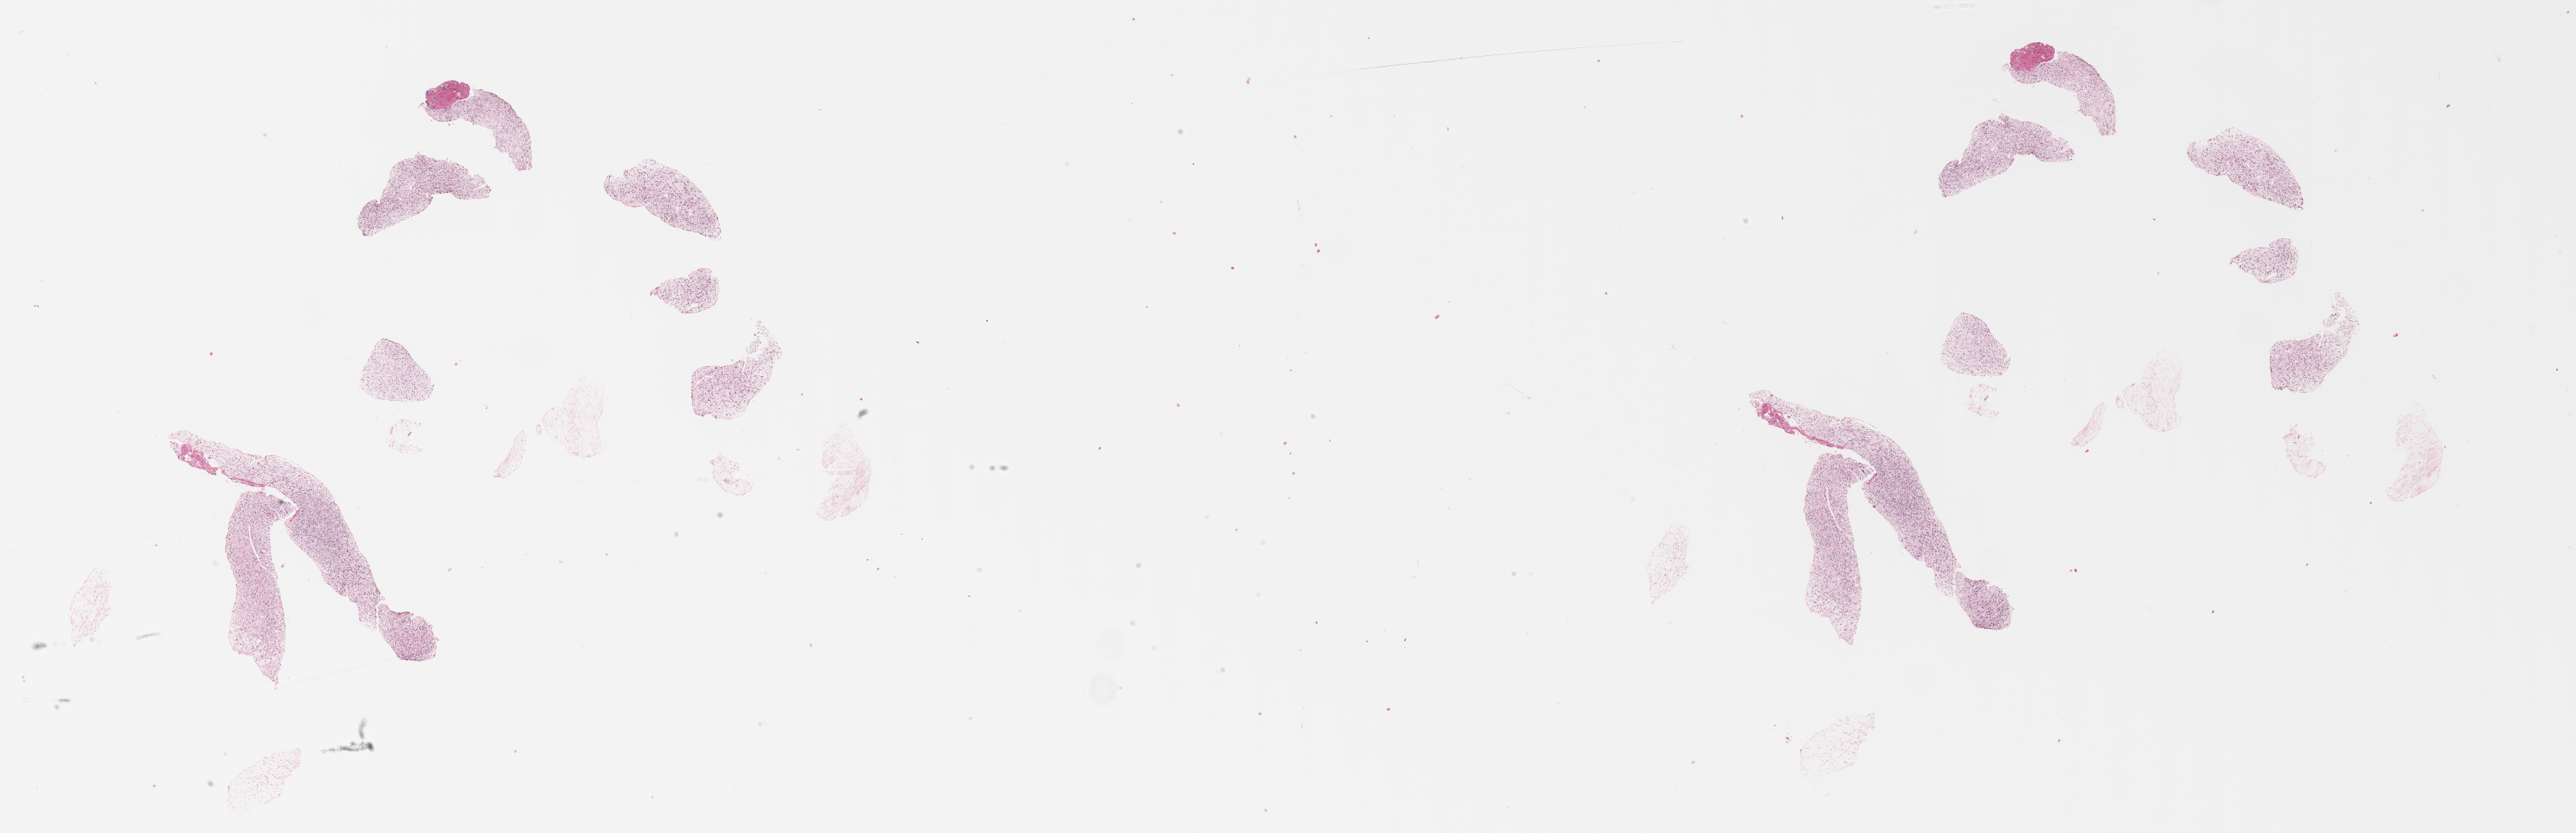
Whole-slide image, hematoxylin and eosin (H&E) stain of tumor tissue — whole scanned area (about 28.7 x 9.3 mm) shown as a low-resolution overview; formalin-fixed, paraffin-embedded (FFPE) tissue. Patient: male, age 9.9 years at diagnosis.
- metastatic status at presentation (as recorded): non-metastatic
- diagnosis: rhabdomyosarcoma; histological classification: embryonal rhabdomyosarcoma
- stage (as recorded): 2